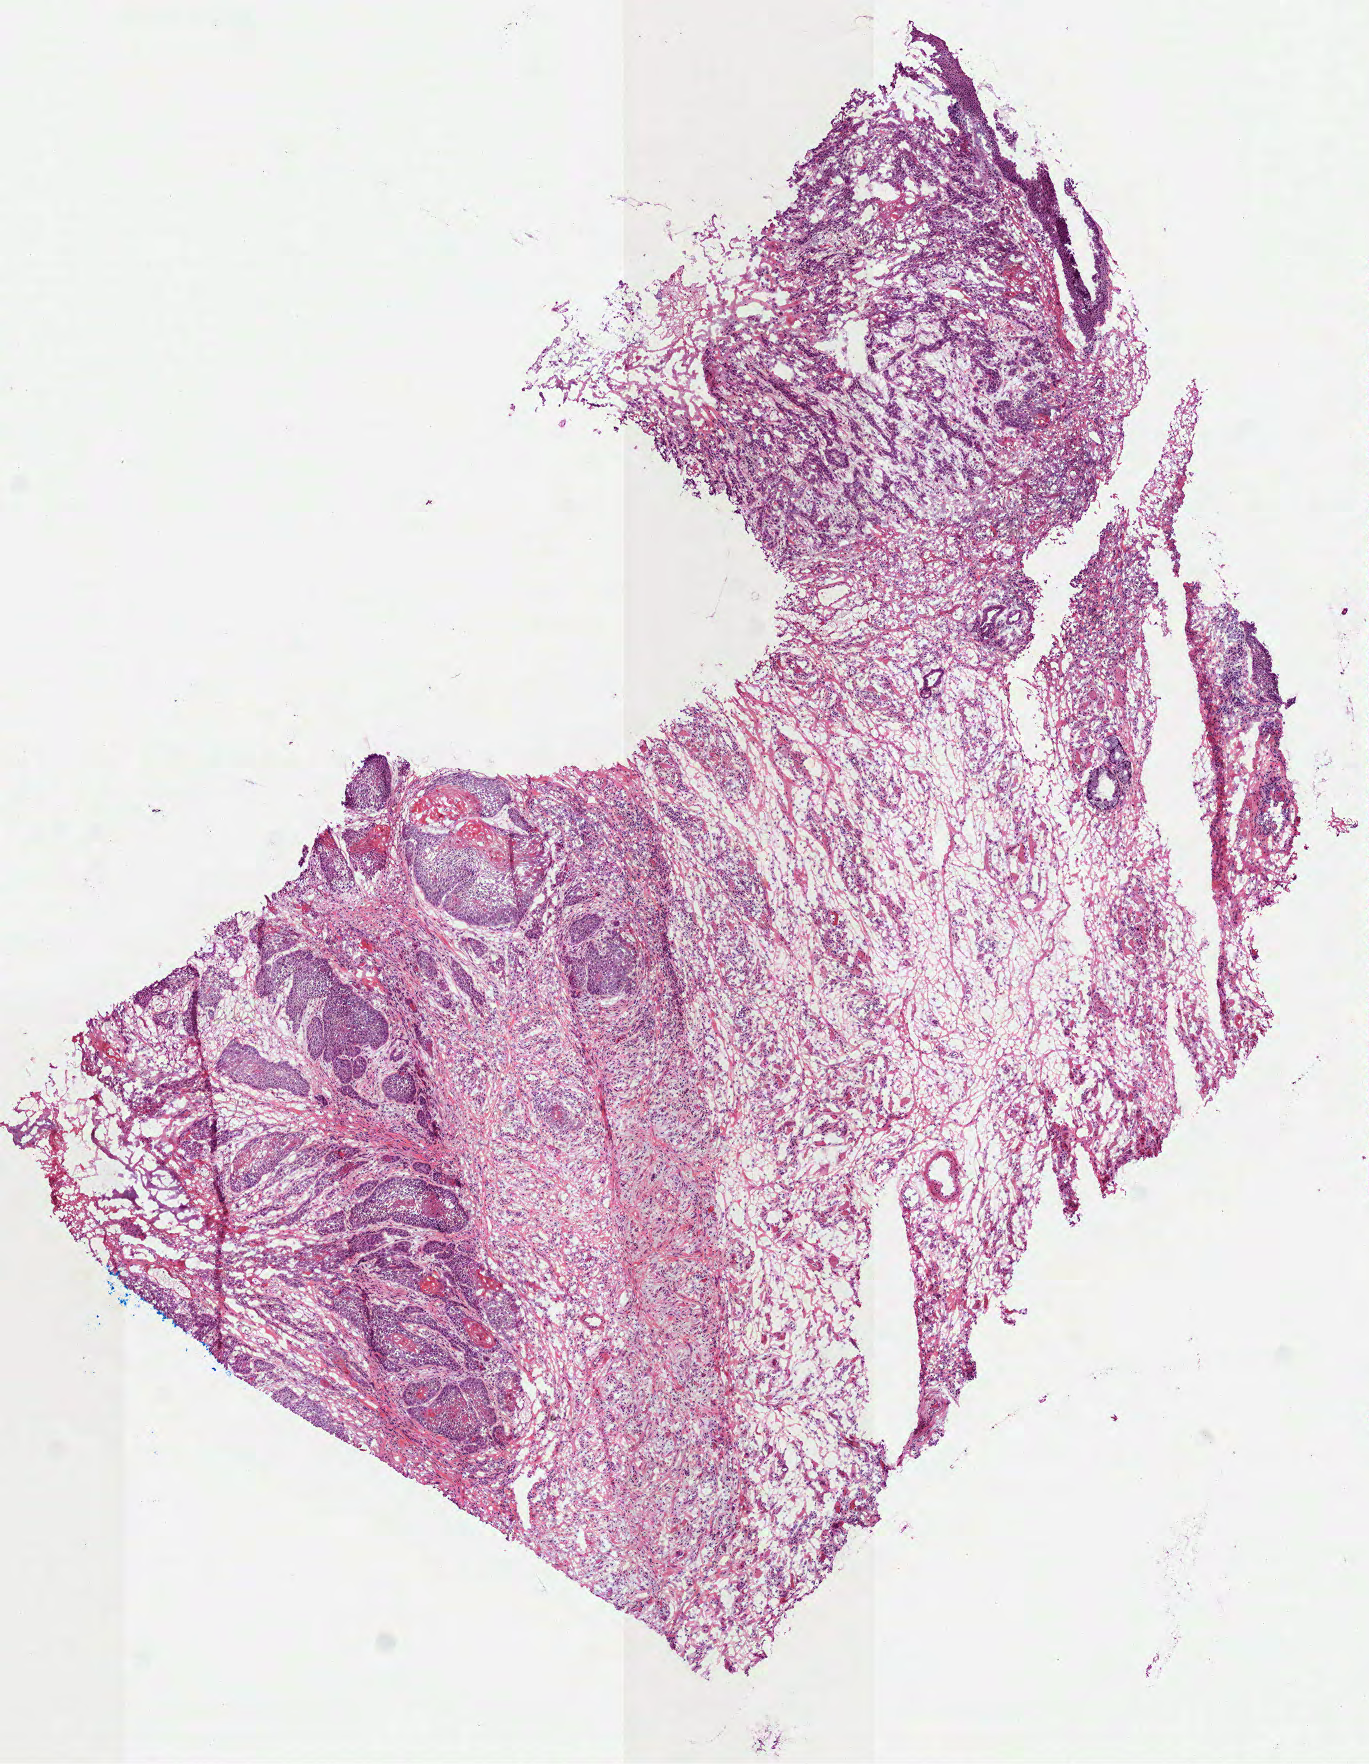
Digitized H&E tissue section (whole slide) — shown as a low-resolution overview of the whole scanned area (about 5.5 x 7.1 mm, acquisition: 40x scan); frozen section; sample: primary tumour, head and neck. Male patient; age at initial diagnosis 62 years. Composition of this section per pathologist review: tumour cells 50%, tumour nuclei 60%.
Pathologic diagnosis: Squamous cell carcinoma, keratinizing, NOS (larynx, NOS).